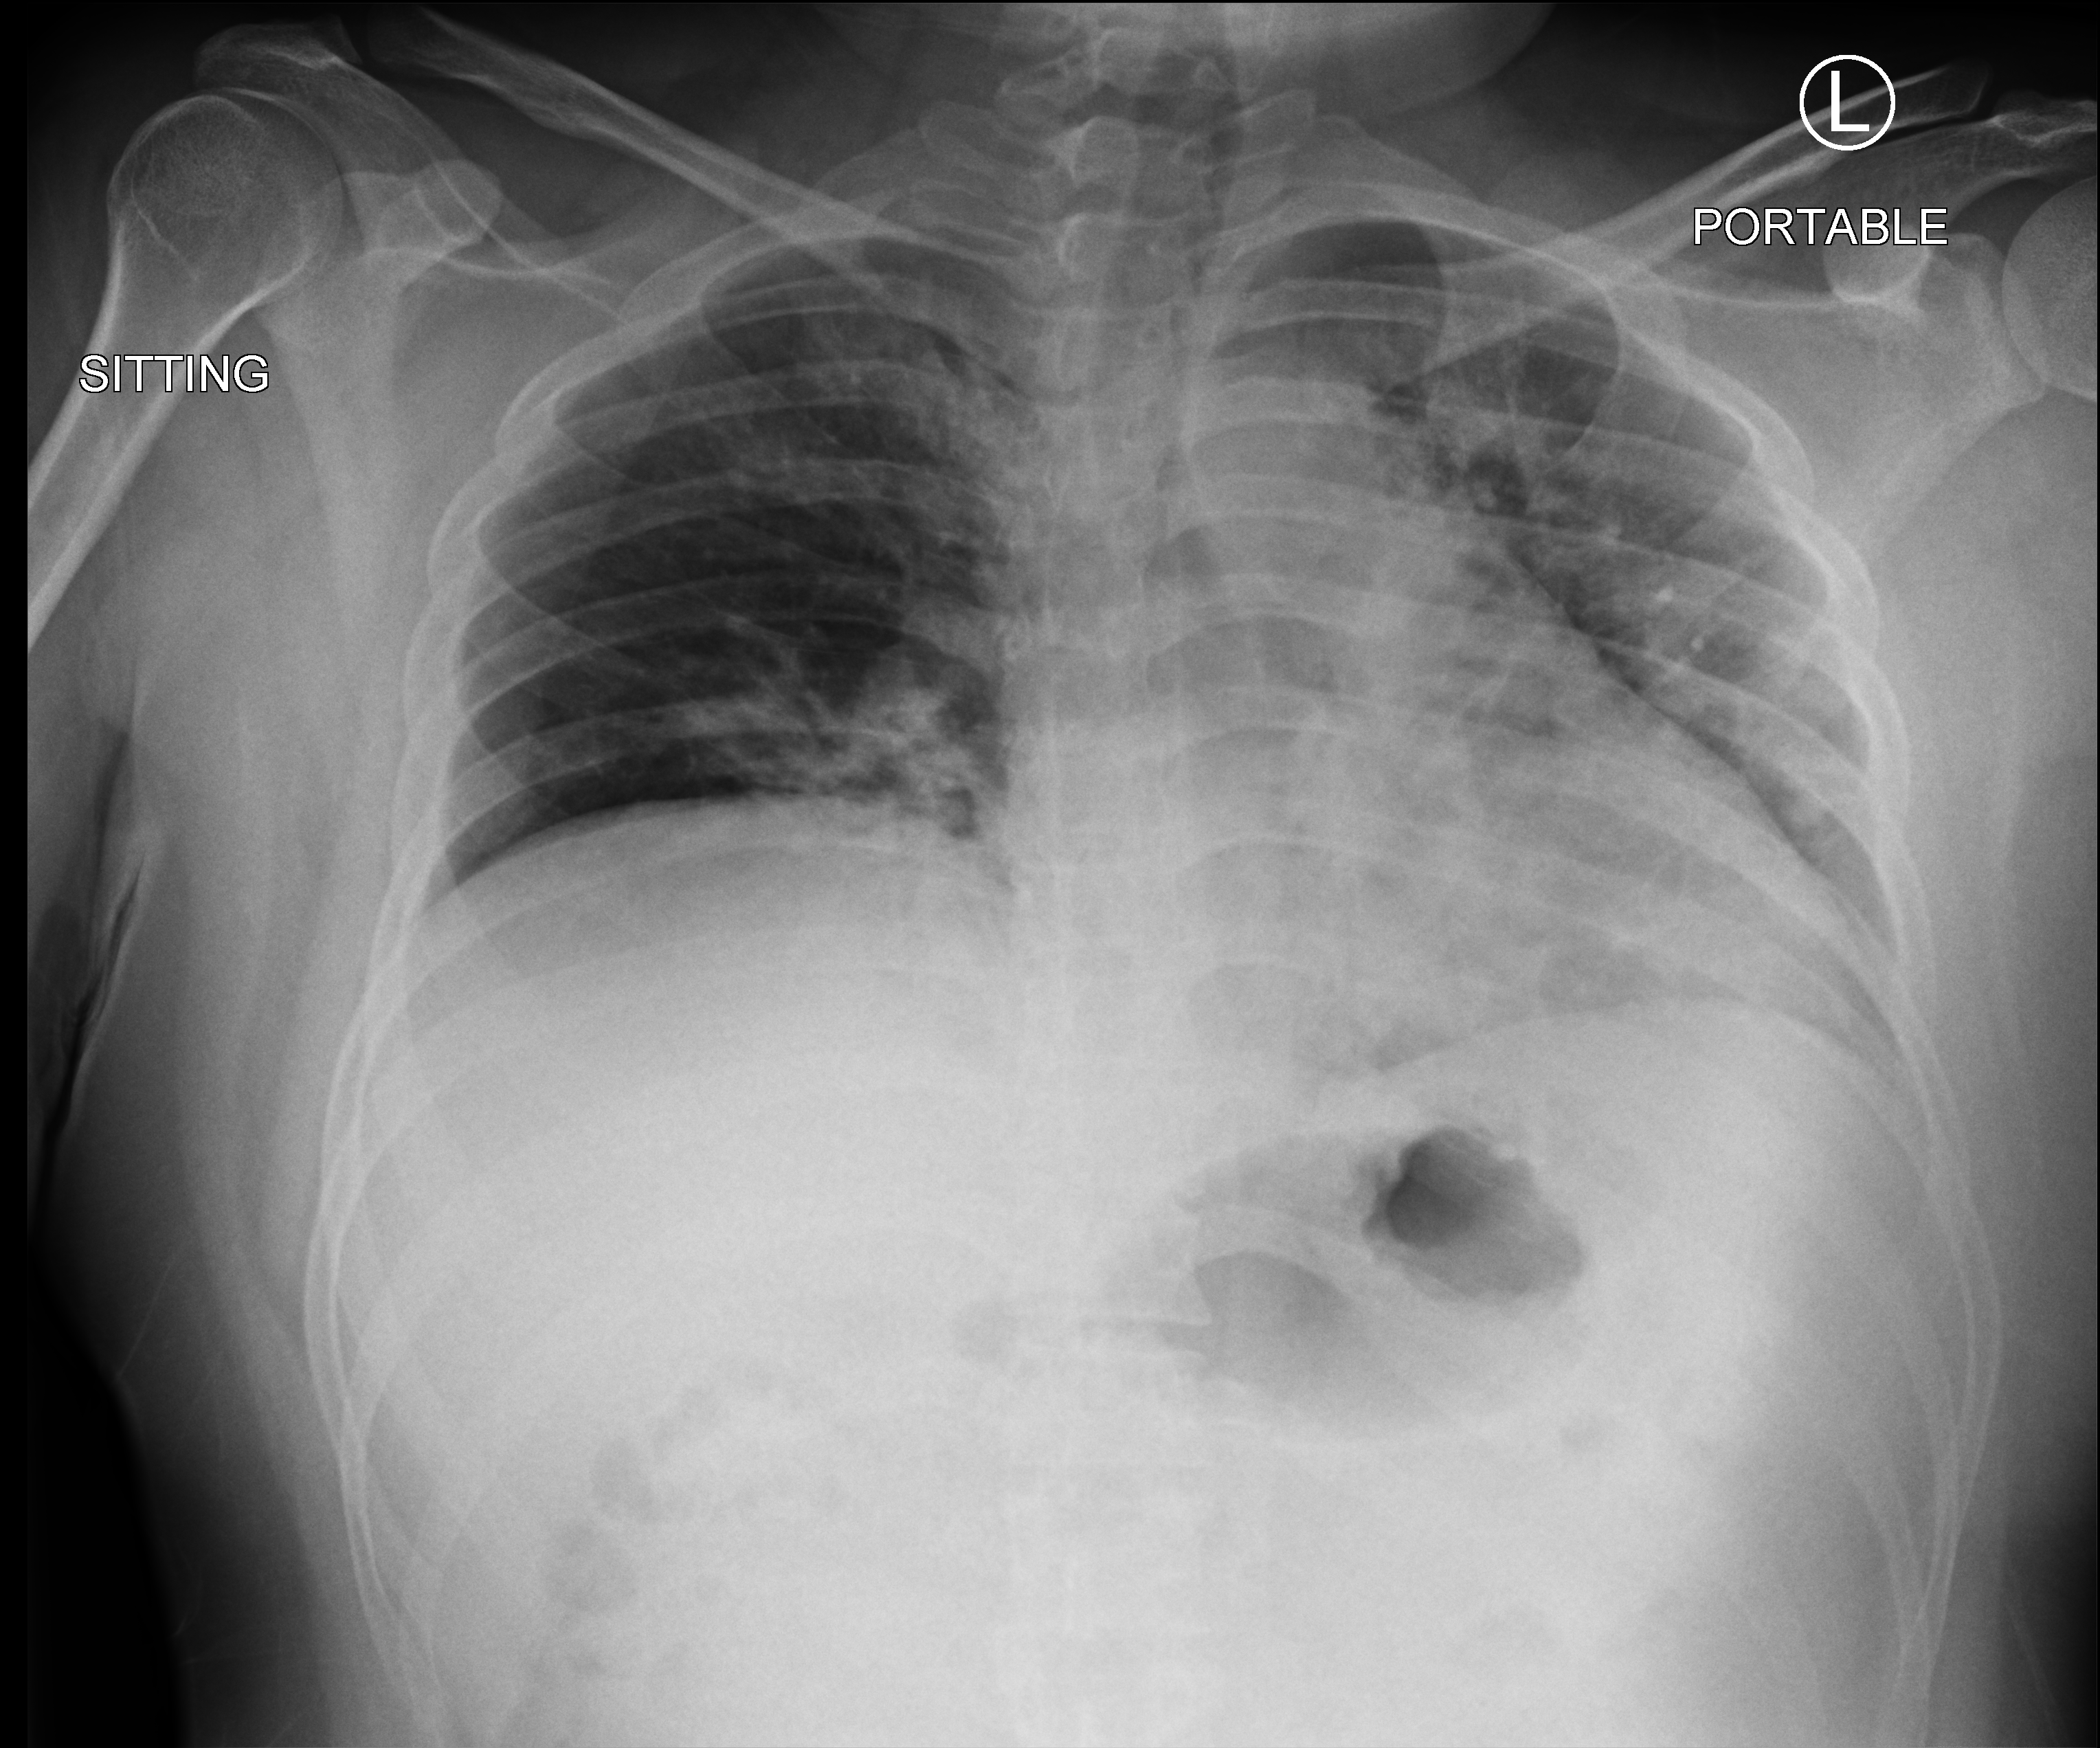
Portable chest radiograph, anteroposterior (AP) projection. Patient hospitalised with COVID-19; male, aged 18–59 years.
Hospital-stay facts (about this admission, not read from this image; timing relative to this image not recorded): diabetes (admission record): no; hypertension (admission record): no.